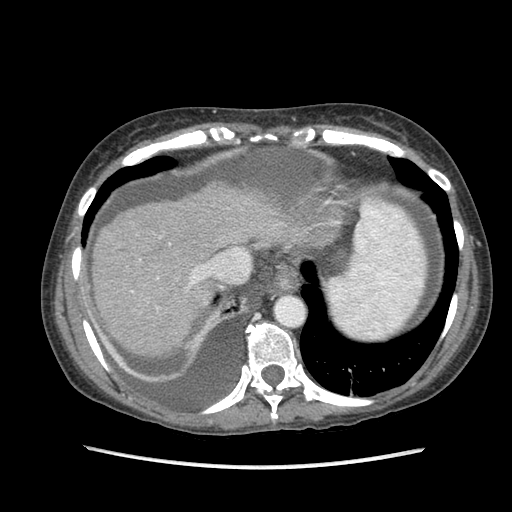
Contrast-enhanced abdominal CT (liver protocol), one axial slice; slice 75 of 87 in the series (ordered by position); reconstruction kernel STANDARD; 120 kVp; soft-tissue window (W 400 / L 40 HU); 2.5 mm slice thickness; 512 × 512 image matrix, field of view 340 × 340 mm. Case-level facts recorded for this patient, not image findings: diagnosis: hepatocellular carcinoma (patient treated with transarterial chemoembolisation; whether this scan precedes or follows treatment is not stated here); TNM stage (as recorded): Stage-IIIB; Child-Pugh class: A; tumour differentiation: no biopsy; tumour nodularity: uninodular.
Annotated regions visible in this slice (semi-automatic segmentation, software-assisted and operator-edited):
- liver parenchyma outside the tumour (the mass and vessels are separate outlines, so this box may not span the whole liver): bounding box <92,182,333,356> (left, top, right, bottom; pixels)
- liver vessels: <131,265,211,292>